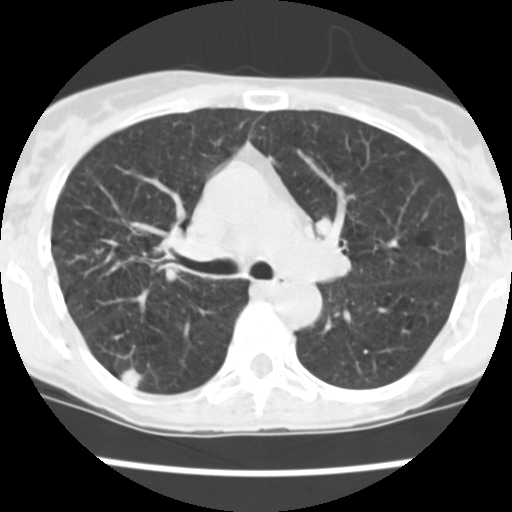
Low-dose screening chest CT, one axial slice. Position 154 of 252 along the scan axis. Reconstruction kernel STANDARD. Lung window (W 1500 / L -600 HU). 2.5 mm slice thickness. 512 × 512 image matrix, field of view 276 × 276 mm.
Outlined on this slice (manually delineated by an expert):
- lesion 1 (tumor, upper lobe of right lung): bounding box [x1, y1, x2, y2] px = [121, 368, 142, 390]